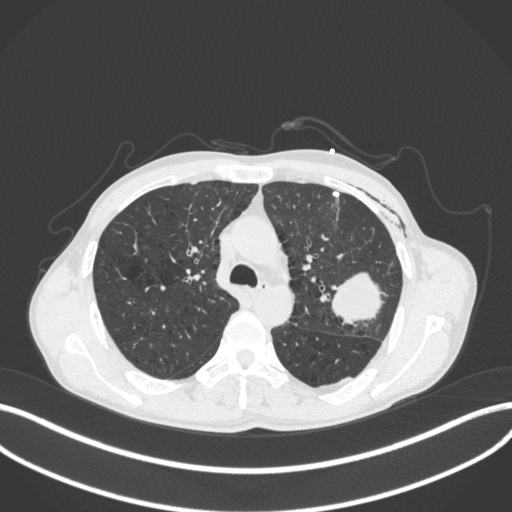
Chest CT, one axial slice; slice 275 of 416 in the series (ordered by position); reconstruction kernel B31f; lung window (W 1500 / L -600 HU); 512 × 512 image matrix, field of view 400 × 400 mm. Male patient, age 58 years. From the clinical record (not read from this slice): clinical TNM (as recorded): T3 N0 M0.
Structures marked on this image (rectangle marked by the reading radiologist):
- lung tumour (recorded histology: adenocarcinoma): bounding box [x1, y1, x2, y2] px = [325, 257, 389, 331]